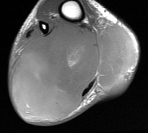
MRI of an extremity soft-tissue mass, one axial slice. Position 31 of 76 along the scan axis. MR volume resampled by the dataset authors to the PET/CT grid (not the native acquisition matrix). 3.27 mm slice thickness. 148 × 133 image matrix, field of view 145 × 130 mm. Male patient. From the clinical record (not read from this slice): histological type: liposarcoma - round cell; grade: high; site of the primary tumour: right calf.
Structures marked on this image (expert contour drawn on MRI and transferred to this co-registered scan by the dataset authors):
- gross tumour volume (mass): bounding box (x1, y1, x2, y2) in pixels: (11, 21, 137, 116)